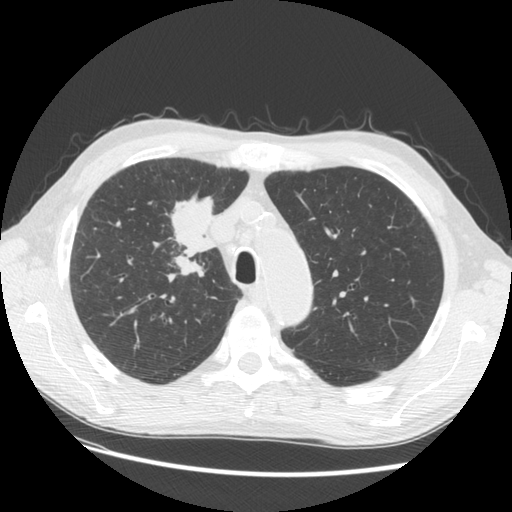
Low-dose screening chest CT, one axial slice; position 101 of 133 along the scan axis; reconstruction kernel STANDARD; lung window (W 1500 / L -600 HU); 2.5 mm slice thickness; 512 × 512 image matrix, field of view 360 × 360 mm.
Outlined on this slice (expert manual segmentation):
- lesion 1 (tumor, hilum of right lung): bounding box [x1, y1, x2, y2] px = [170, 191, 217, 277]